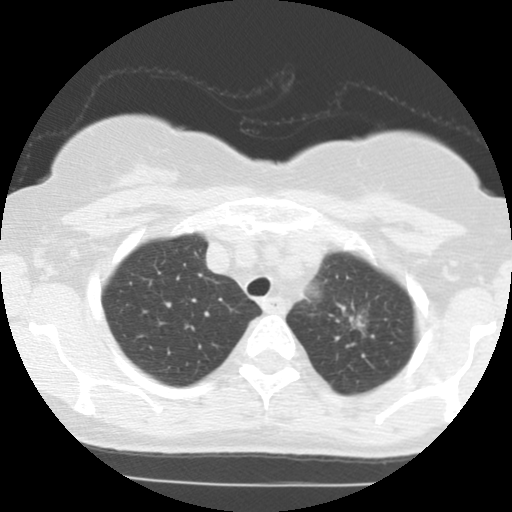
Chest CT (low-dose screening protocol), one axial image, first (baseline) screen, lung window (W 1500 / L -600 HU), standard (soft-tissue) reconstruction kernel (STANDARD), slice 99 of 123 in the series. Female, age 61 years at enrolment. Former smoker at enrolment.
- Expert reader's lesion annotation, bounding box [x1, y1, x2, y2] px = [320, 297, 388, 350].
- The screening reader recorded 2 non-calcified nodules or masses ≥4 mm on this exam (right lower lobe, left upper lobe); which of them this box marks is not recorded.
- Official screen result: positive, change unspecified: nodule(s) >= 4 mm or enlarging nodule(s), mass(es), or other non-specific abnormalities suspicious for lung cancer.
- Participant outcome: lung cancer diagnosed 79 days after this screen — adenocarcinoma, NOS, left upper lobe, stage IIIB (AJCC 6th edition), 15 mm at pathology.